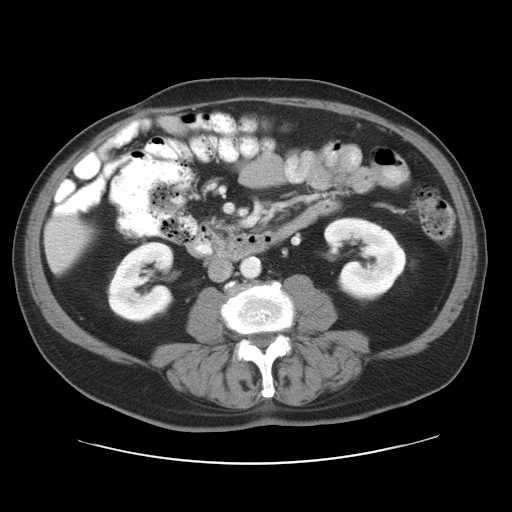
Contrast-enhanced abdominal CT, one axial slice; slice 8 of 28 in the series (ordered by position); reconstruction kernel STANDARD; intravenous contrast given; soft-tissue window (W 400 / L 40 HU); 7.5 mm slice thickness; 512 × 512 image matrix. Male patient, age 74 years. Case-level facts recorded for this patient, not image findings: diagnosis: colorectal cancer liver metastases, imaged before liver resection; multiple liver metastases: no; largest metastasis: 5 cm; disease in both lobes: no.
Outlined on this slice (expert manual segmentation):
- liver: bounding box [x1, y1, x2, y2] px = [47, 222, 86, 268]
- planned liver remnant (the part of the liver to remain after resection): [47, 222, 87, 268]